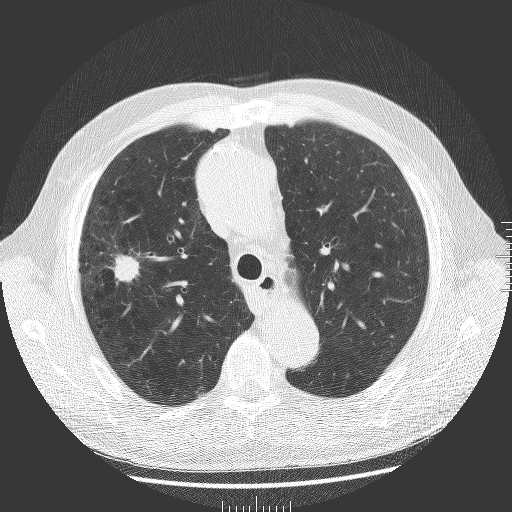
Low-dose screening chest CT, one axial slice; slice 133 of 181 in the series (ordered by position); 120 kVp; lung window (W 1500 / L -600 HU); 512 × 512 image matrix.
Annotated regions visible in this slice (manually delineated by an expert):
- lesion 1 (tumor, upper lobe of right lung): box from (x=112, y=255) to (x=139, y=282) px